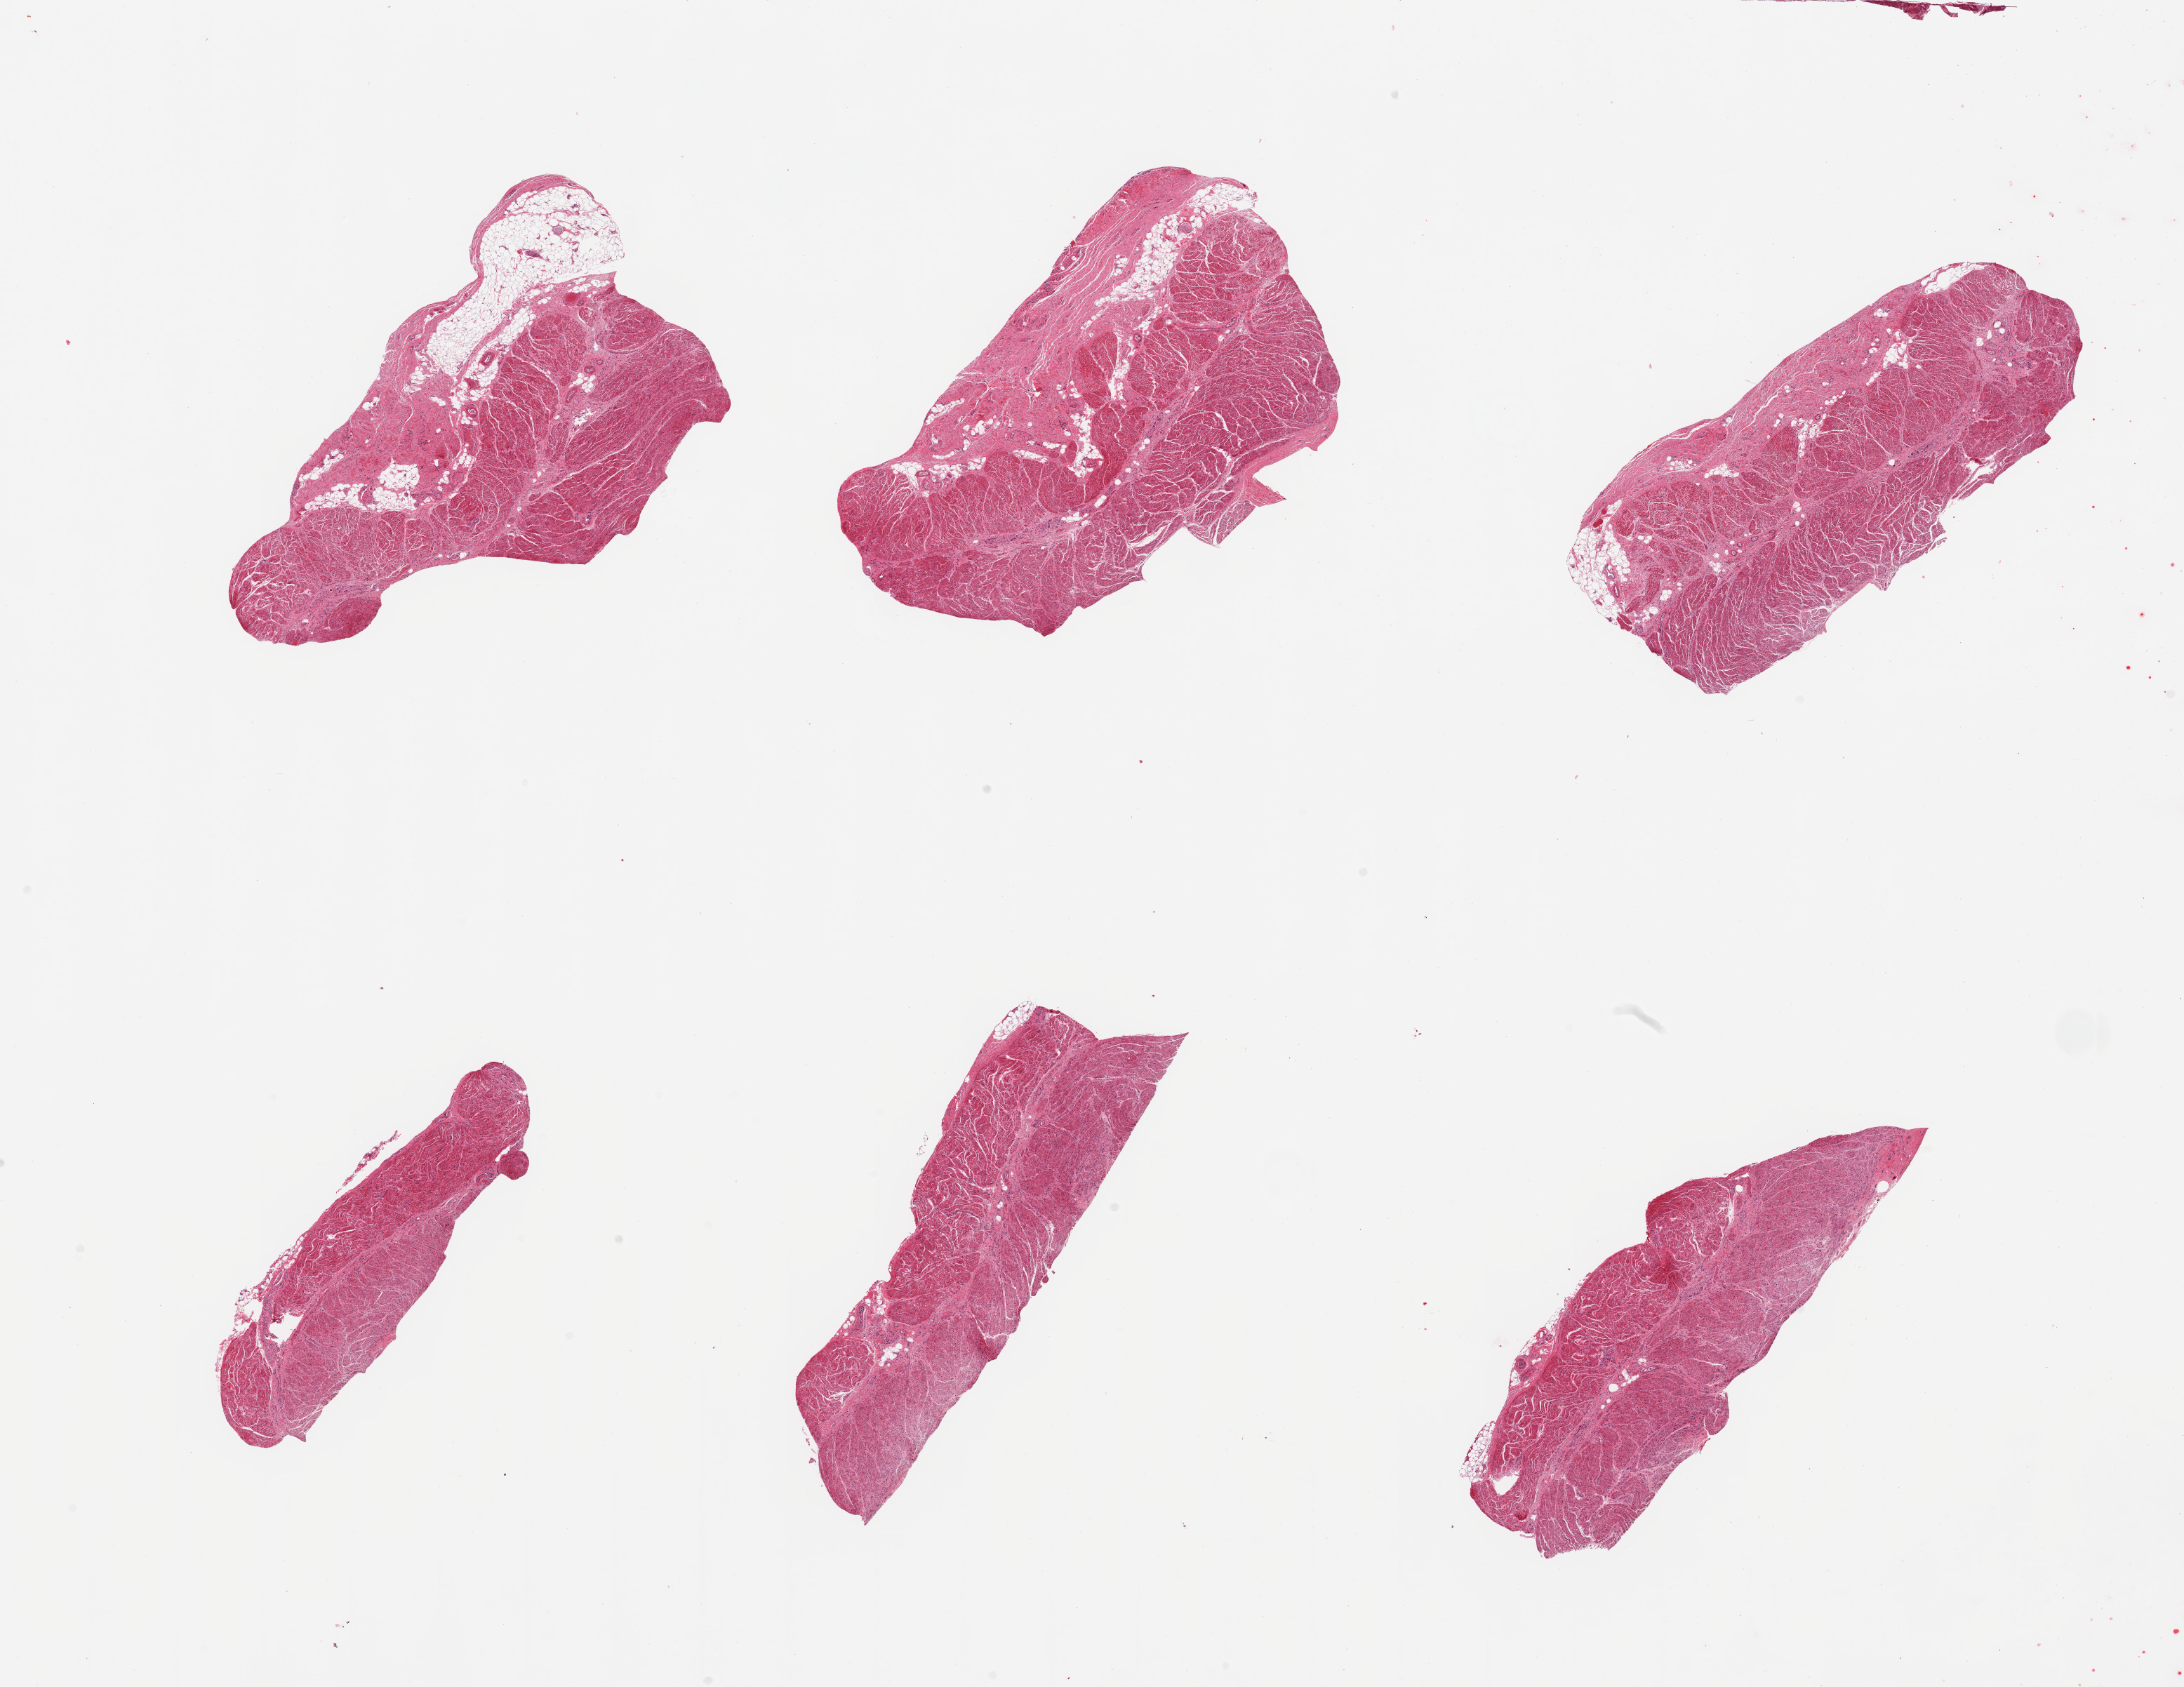
Digitized H&E-stained section, brightfield — shown as a low-resolution overview of the whole scanned area (about 24.6 x 19.0 mm, slide scanned at 20x). PAXgene-fixed paraffin-embedded (PFPE) section. Sampled site (target tissue): gastroesophageal junction. Donor tissue sample. Donor sex: male.
Reviewer comment on this tissue sample: 6 pieces, confirmed target muscularis.